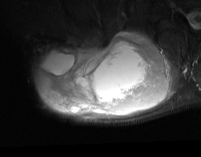
MRI of an extremity soft-tissue mass, one axial slice; slice 46 of 74 in the series (ordered by position); STIR; MR volume resampled by the dataset authors to the PET/CT grid (not the native acquisition matrix); 3.27 mm slice thickness; 201 × 157 image matrix, field of view 196 × 153 mm. Male patient. Case-level facts recorded for this patient, not image findings: histological type: pleiomorphic spindle cell undifferentiated; grade: high; site of the primary tumour: right parascapusular.
Outlined on this slice (expert contour drawn on MRI and transferred to this co-registered scan by the dataset authors):
- gross tumour volume including surrounding oedema: bounding box (x1, y1, x2, y2) in pixels: (35, 27, 178, 120)
- gross tumour volume (mass): (39, 32, 169, 115)